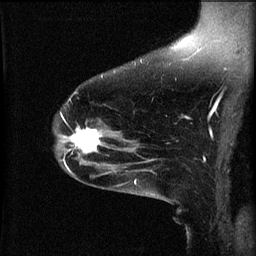
Breast MRI (dynamic contrast-enhanced), one sagittal slice. 3 images stored at this slice position (order not interpretable as contrast timing). 1.5 T. TE 4.2 ms, TR 8.2 ms. 2 mm slice thickness. 256 × 256 image matrix, field of view 200 × 200 mm. Female patient, age 49 years.
Annotated regions visible in this slice (semi-automatic segmentation, software-assisted and operator-edited):
- analysis volume of interest (the breast-tissue region the enhancement analysis was run in; not a lesion): box from (x=66, y=124) to (x=113, y=159) px
- tumour enhancement mask (voxels above the 70 % enhancement threshold inside the analysis volume of interest): (x=70, y=128)–(x=103, y=155)